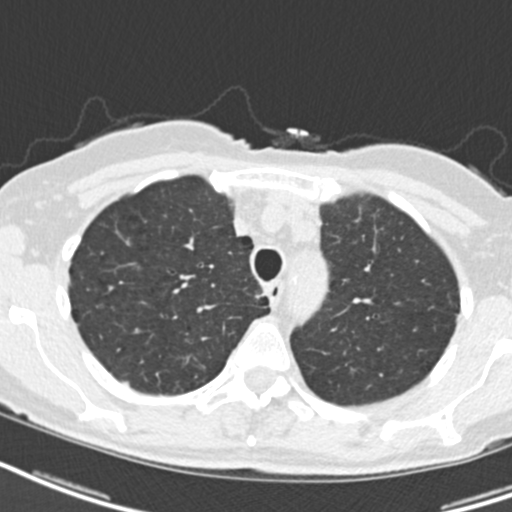
Low-dose screening chest CT, axial slice, baseline screening round, lung window (W 1500 / L -600 HU), 2 mm slice thickness, standard (soft-tissue) reconstruction kernel (B30f), 120 kVp. Female, age 68 years at enrolment.
Lesion marked by an expert reader, bounding box [x1, y1, x2, y2] px = [248, 285, 273, 313]. Screening reader's record for this exam: no non-calcified nodule ≥4 mm recorded. Participant outcome: lung cancer diagnosed 807 days after this screen — squamous cell carcinoma, NOS, right upper lobe, mediastinum, poorly differentiated (G3), stage IIIB (AJCC 6th edition), 43 mm at pathology.